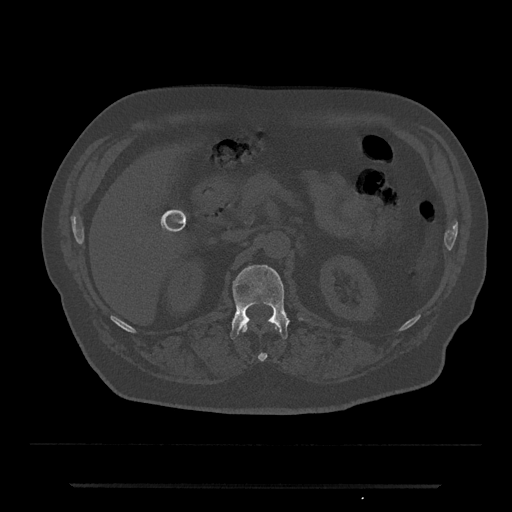
CT including the spine, one axial slice; position 551 of 797 along the scan axis; reconstruction kernel Br40s/3; bone window (W 1800 / L 400 HU); 512 × 512 image matrix, field of view 434 × 434 mm. Patient: male, 80 years. From the clinical record (not read from this slice): primary cancer: prostate; vertebrae with lytic lesions (as recorded): L1, T11.
Outlined on this slice (semi-automatically segmented with operator editing):
- L1 vertebra: box from (x=230, y=265) to (x=303, y=339) px
- T12 vertebra: (x=242, y=325)–(x=279, y=361)